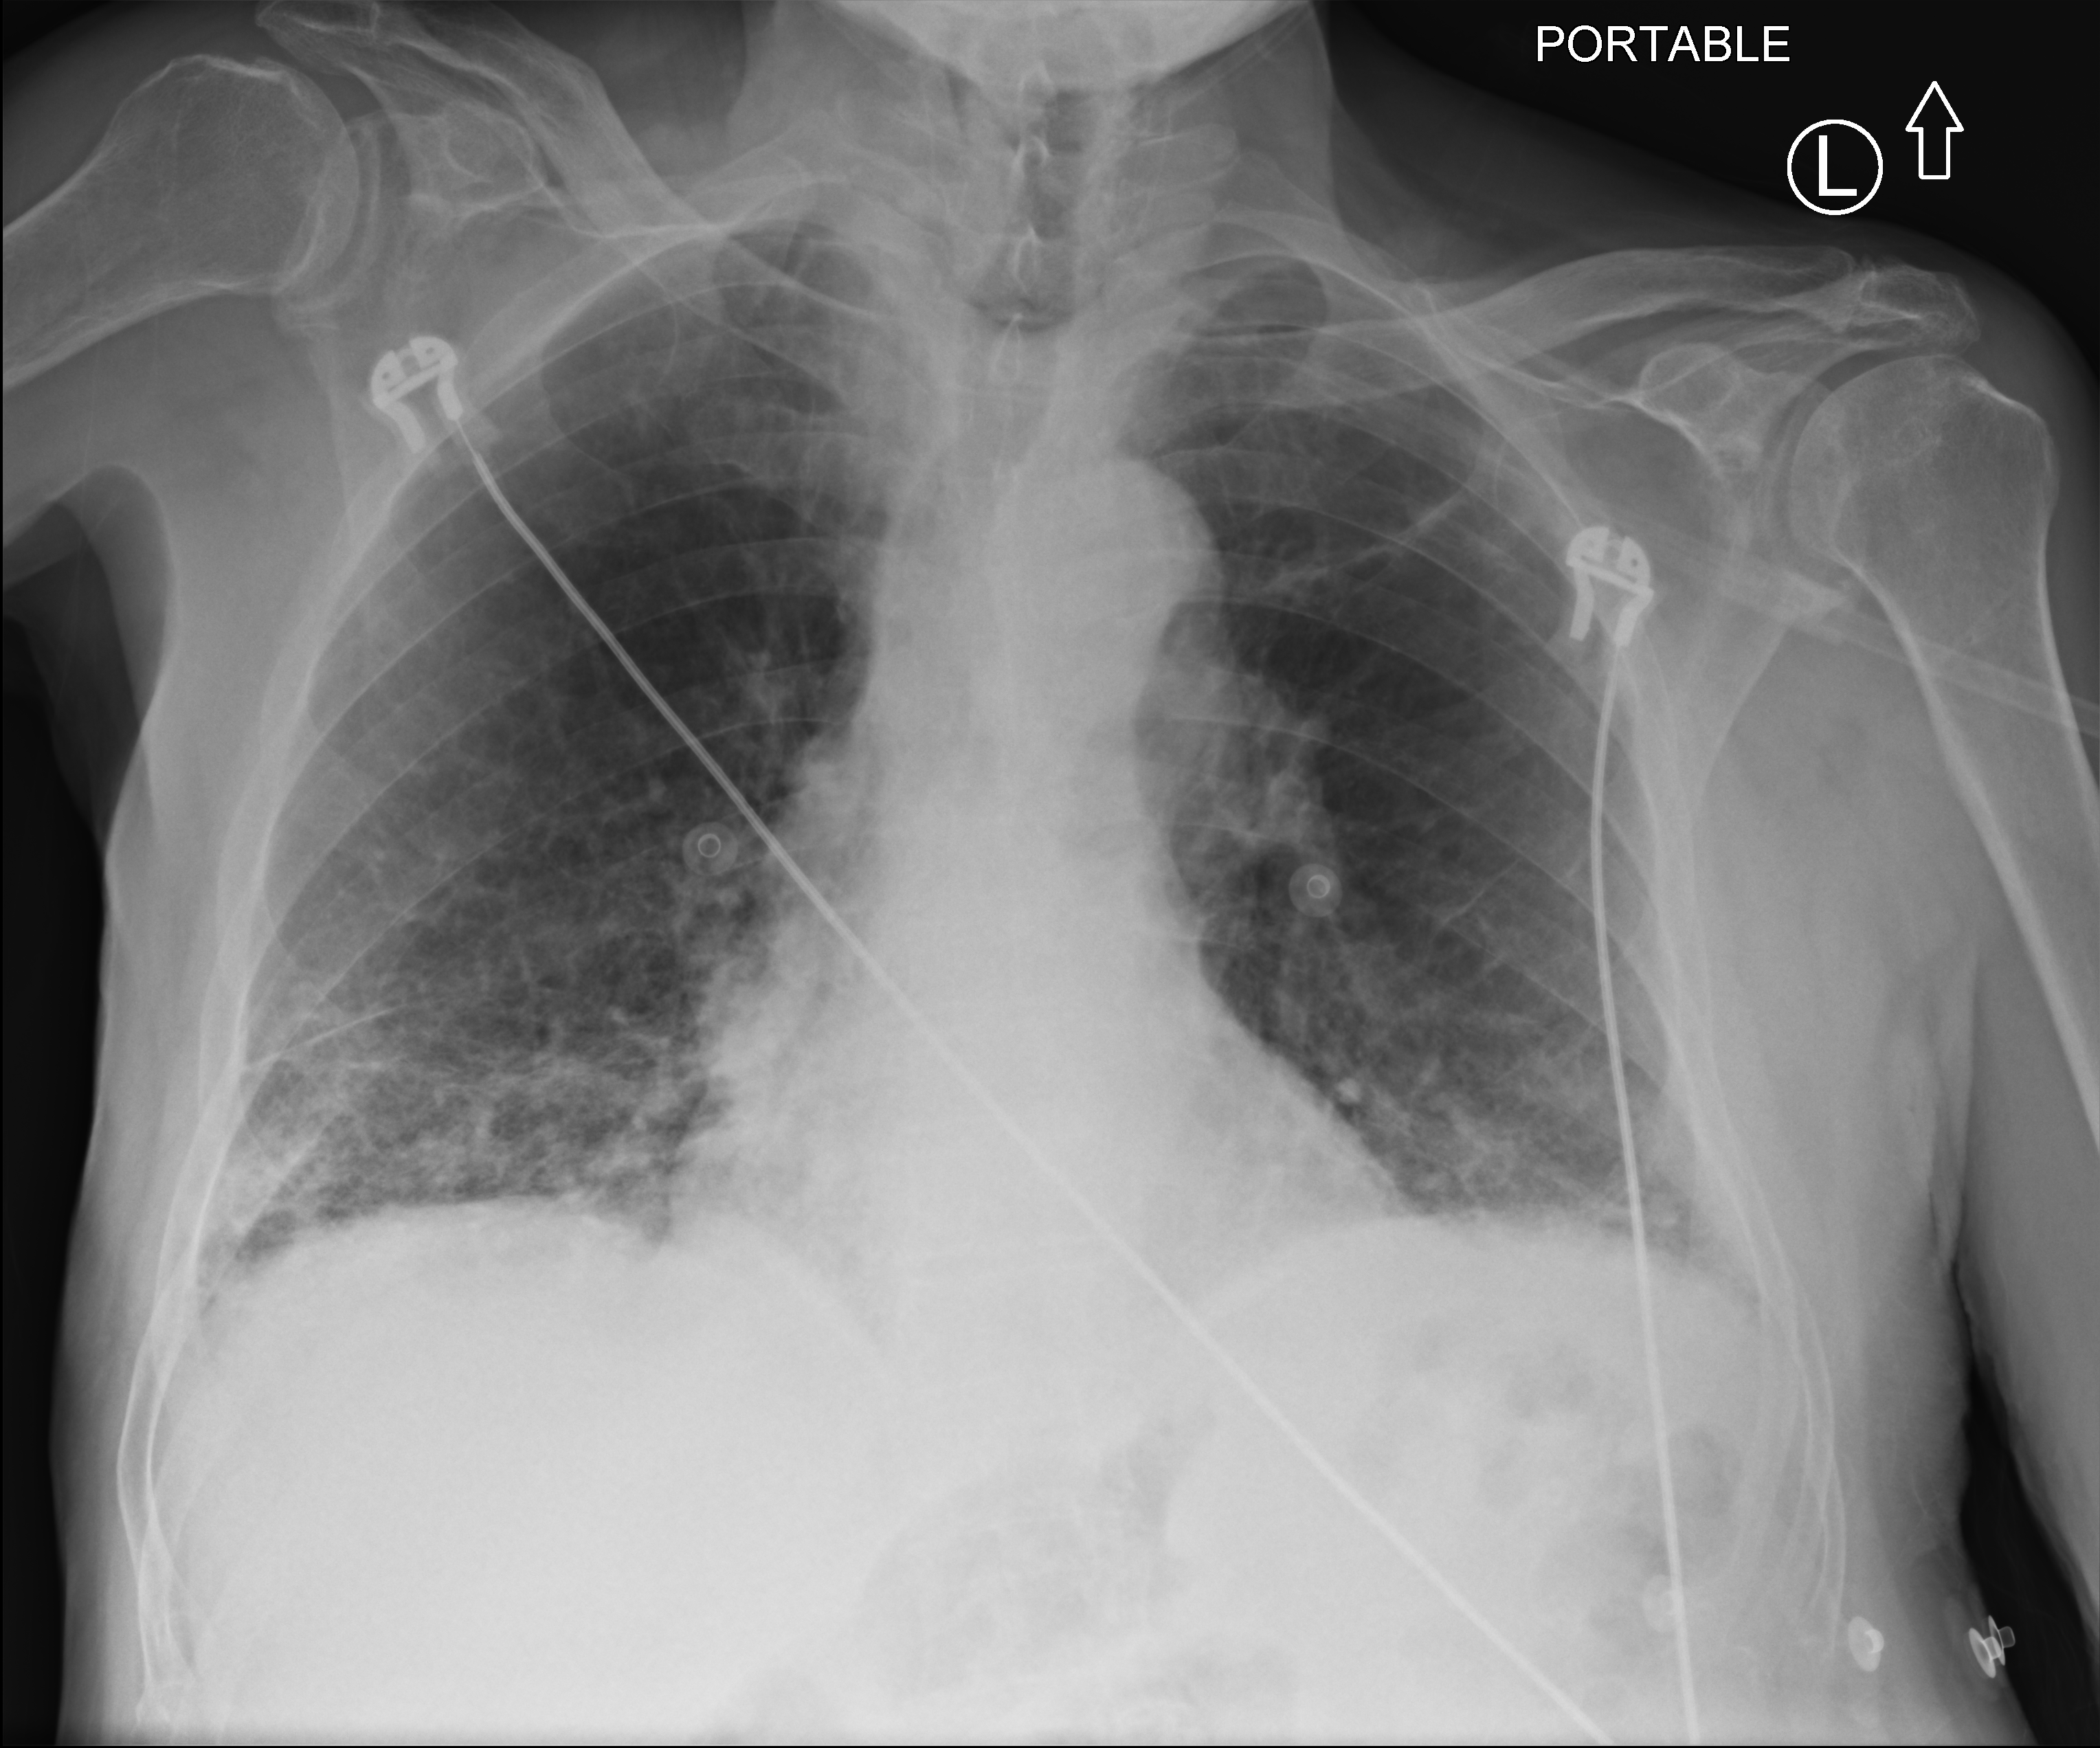
Chest X-ray (portable). Patient hospitalised with COVID-19; male, aged 75–90 years.
Admission-level facts for this patient (not findings on this image; timing relative to this image not recorded): mechanically ventilated during this hospital stay: no.